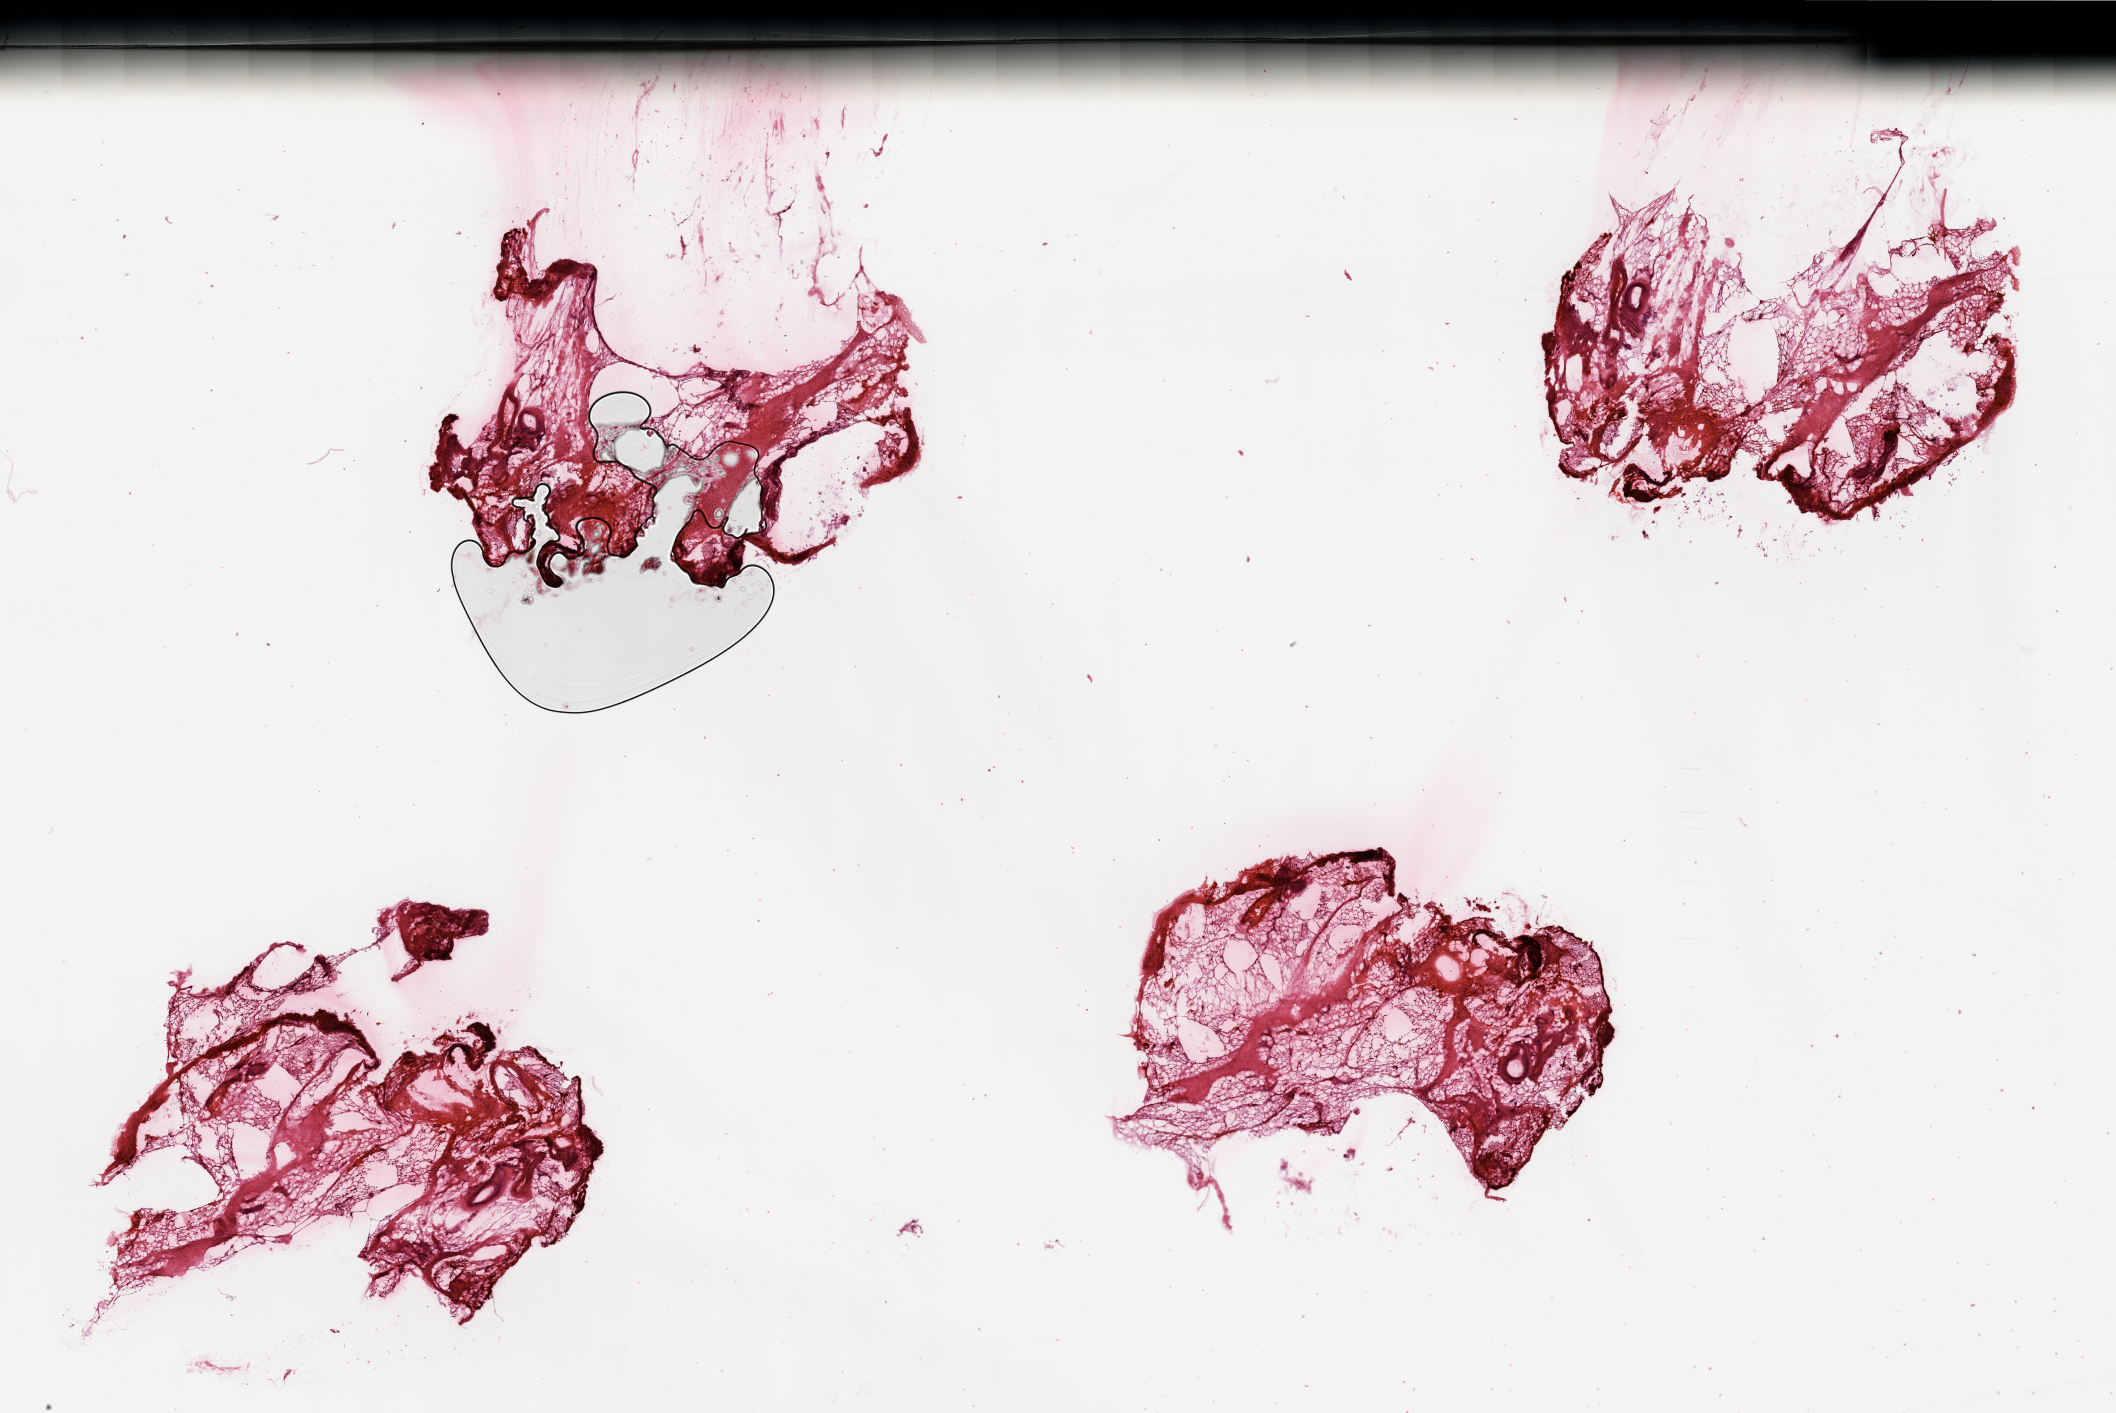
Digitized Hematoxylin and eosin (H&E) stained tissue section (whole slide) — shown as a low-resolution overview of the whole scanned area (about 33.5 x 22.4 mm, from a 20x scan); normal (non-tumour) tissue sample, sampled site: oral cavity. 63-year-old male patient.
This section: normal (non-tumour) tissue from the same patient. Patient diagnosis: Squamous cell carcinoma, NOS (overlapping lesion of lip, oral cavity and pharynx).